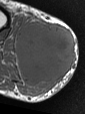
MRI of an extremity soft-tissue mass, one axial slice; slice 23 of 47 in the series (ordered by position); MR volume resampled by the dataset authors to the PET/CT grid (not the native acquisition matrix); 3.27 mm slice thickness; 85 × 114 image matrix, field of view 83 × 111 mm. Male patient. From the clinical record (not read from this slice): histological type: pleiomorphic liposarcoma; grade: high; site of the primary tumour: right calf.
Structures marked on this image (expert contour drawn on MRI and transferred to this co-registered scan by the dataset authors):
- gross tumour volume including surrounding oedema: bounding box <15,14,75,95> (left, top, right, bottom; pixels)
- gross tumour volume (mass): <15,21,75,81>